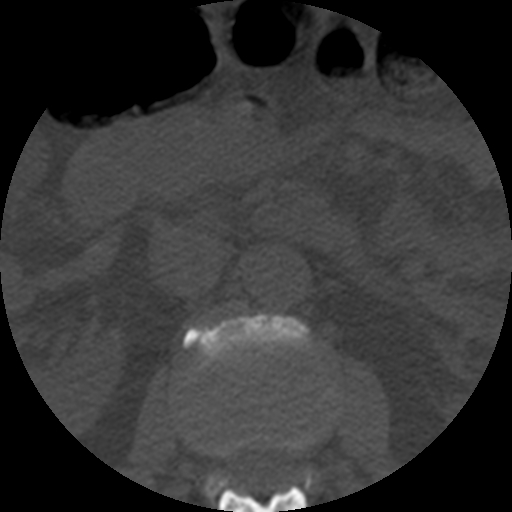
CT including the spine, one axial slice. Position 170 of 508 along the scan axis. Bone window (W 1800 / L 400 HU). 1.25 mm slice thickness. 512 × 512 image matrix, field of view 160 × 160 mm. Patient age 57 years. Case-level facts recorded for this patient, not image findings: primary cancer: prostate.
Structures marked on this image (semi-automatic segmentation, software-assisted and operator-edited):
- L1 vertebra: bounding box (x1, y1, x2, y2) in pixels: (218, 436, 308, 512)
- L2 vertebra: (183, 313, 313, 502)